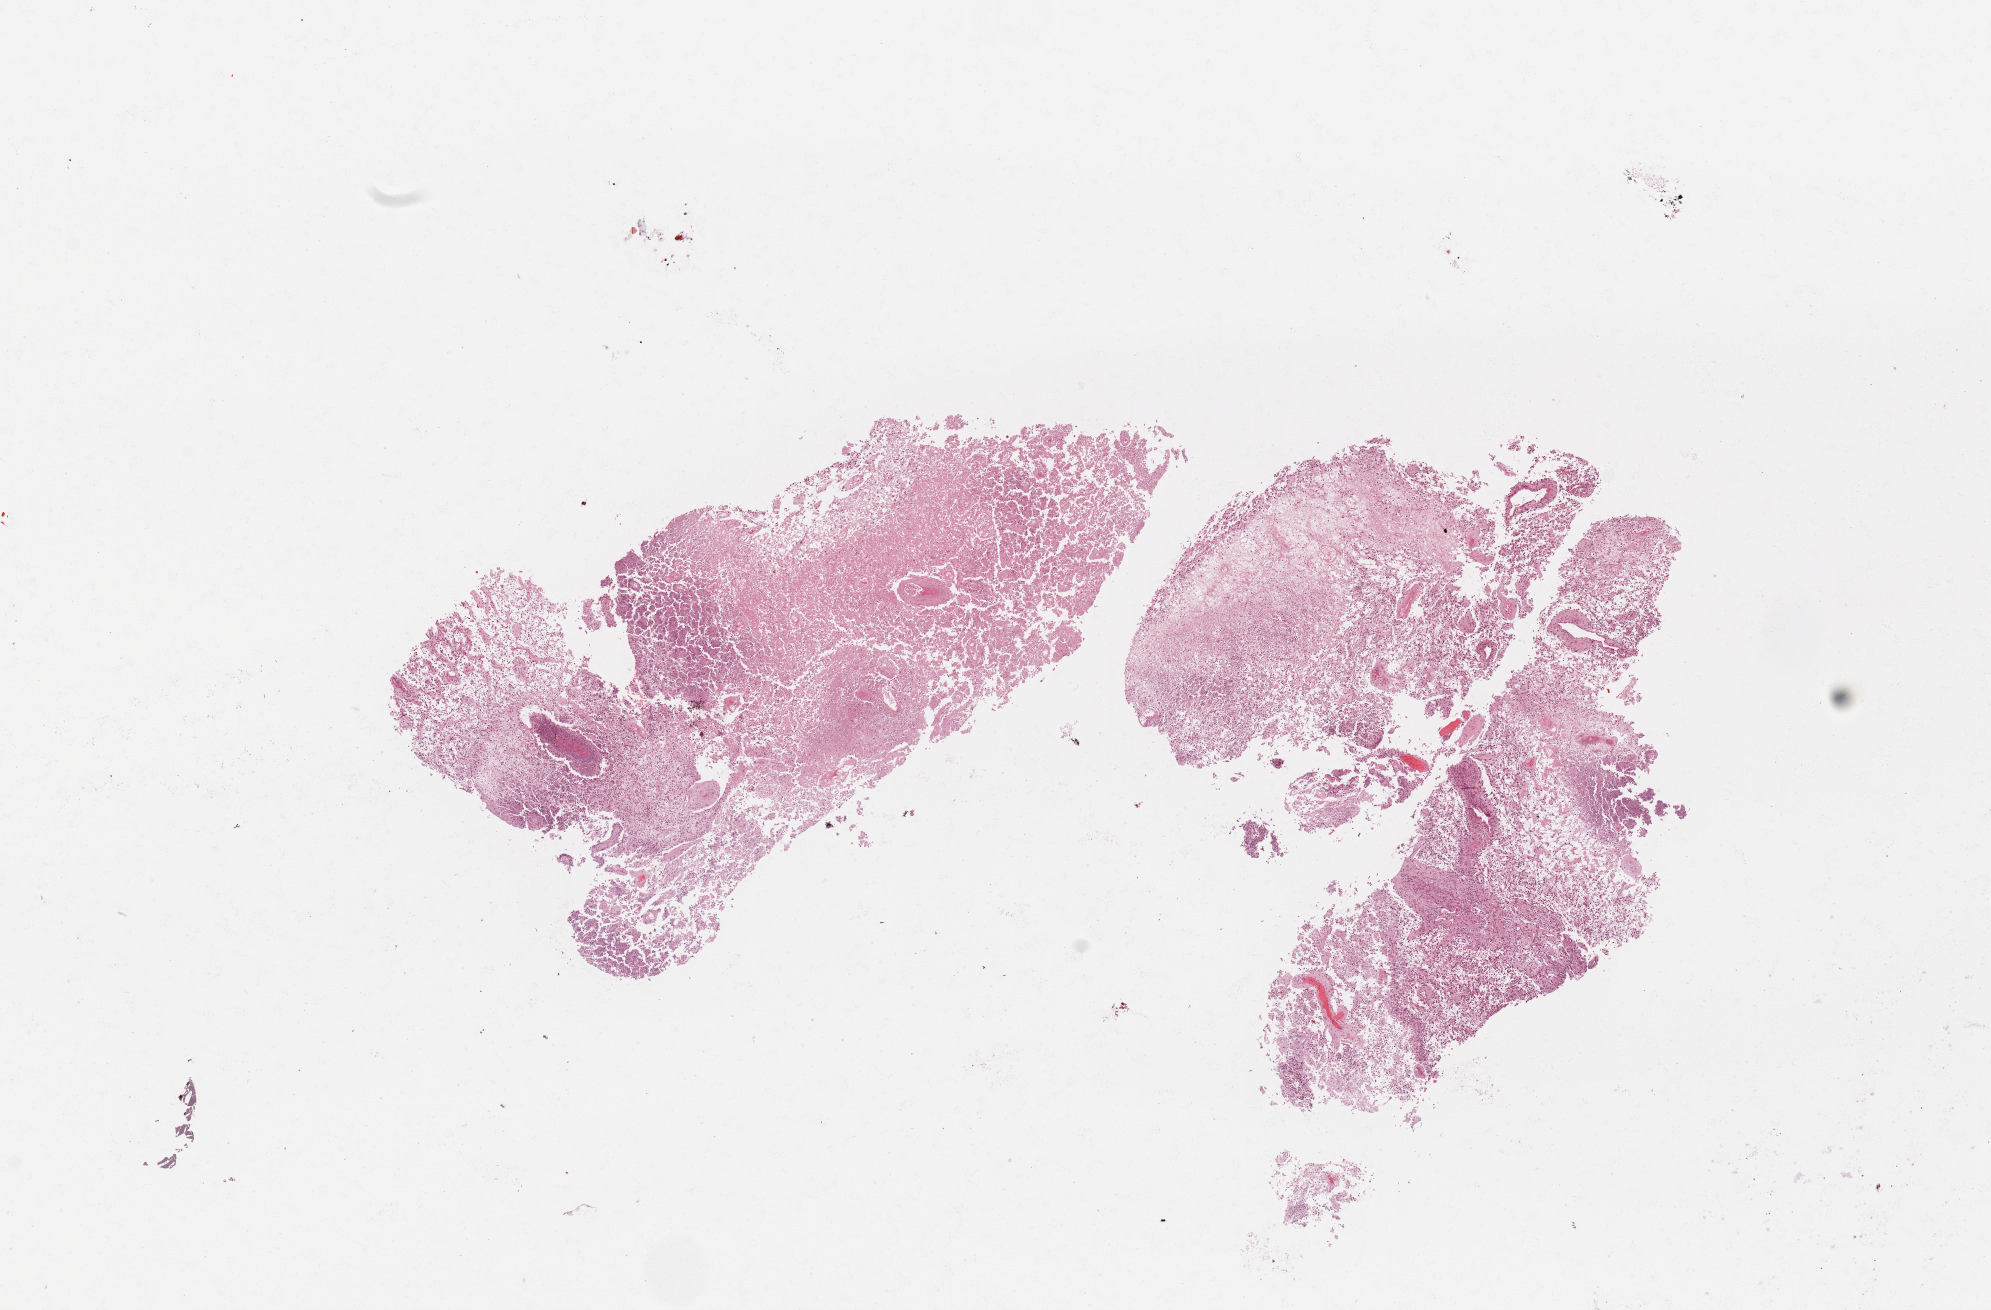
H&E whole-slide image — whole scanned area (about 15.8 x 10.4 mm, acquisition: 20x scan) shown as a low-resolution overview; brain, tumour tissue. 44-year-old male patient.
• primary tumour site (as recorded): frontal lobe
• diagnosis: Glioblastoma